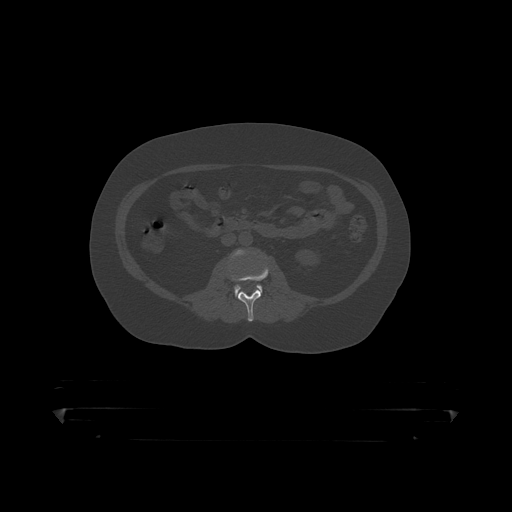
CT including the spine, one axial slice; slice 107 of 390 in the series (ordered by position); reconstruction kernel STANDARD; bone window (W 1800 / L 400 HU); 1.25 mm slice thickness; 512 × 512 image matrix, field of view 650 × 650 mm. Male patient, age 60 years. From the clinical record (not read from this slice): primary cancer: prostate.
Structures marked on this image (semi-automatically segmented with operator editing):
- L2 vertebra: bounding box <229,263,270,319> (left, top, right, bottom; pixels)
- L3 vertebra: <231,250,263,296>